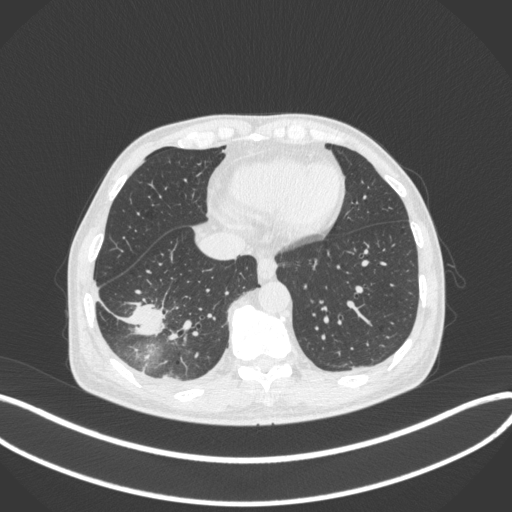
Chest CT, one axial slice; slice 103 of 385 in the series (ordered by position); reconstruction kernel B31f; 120 kVp; lung window (W 1500 / L -600 HU); 512 × 512 image matrix. Male patient, age 64 years. From the clinical record (not read from this slice): clinical TNM (as recorded): T3 N0 M0; histopathological grade: G2-3.
Outlined on this slice (bounding box drawn by a radiologist):
- lung tumour (recorded histology: adenocarcinoma): box from (x=126, y=290) to (x=168, y=340) px